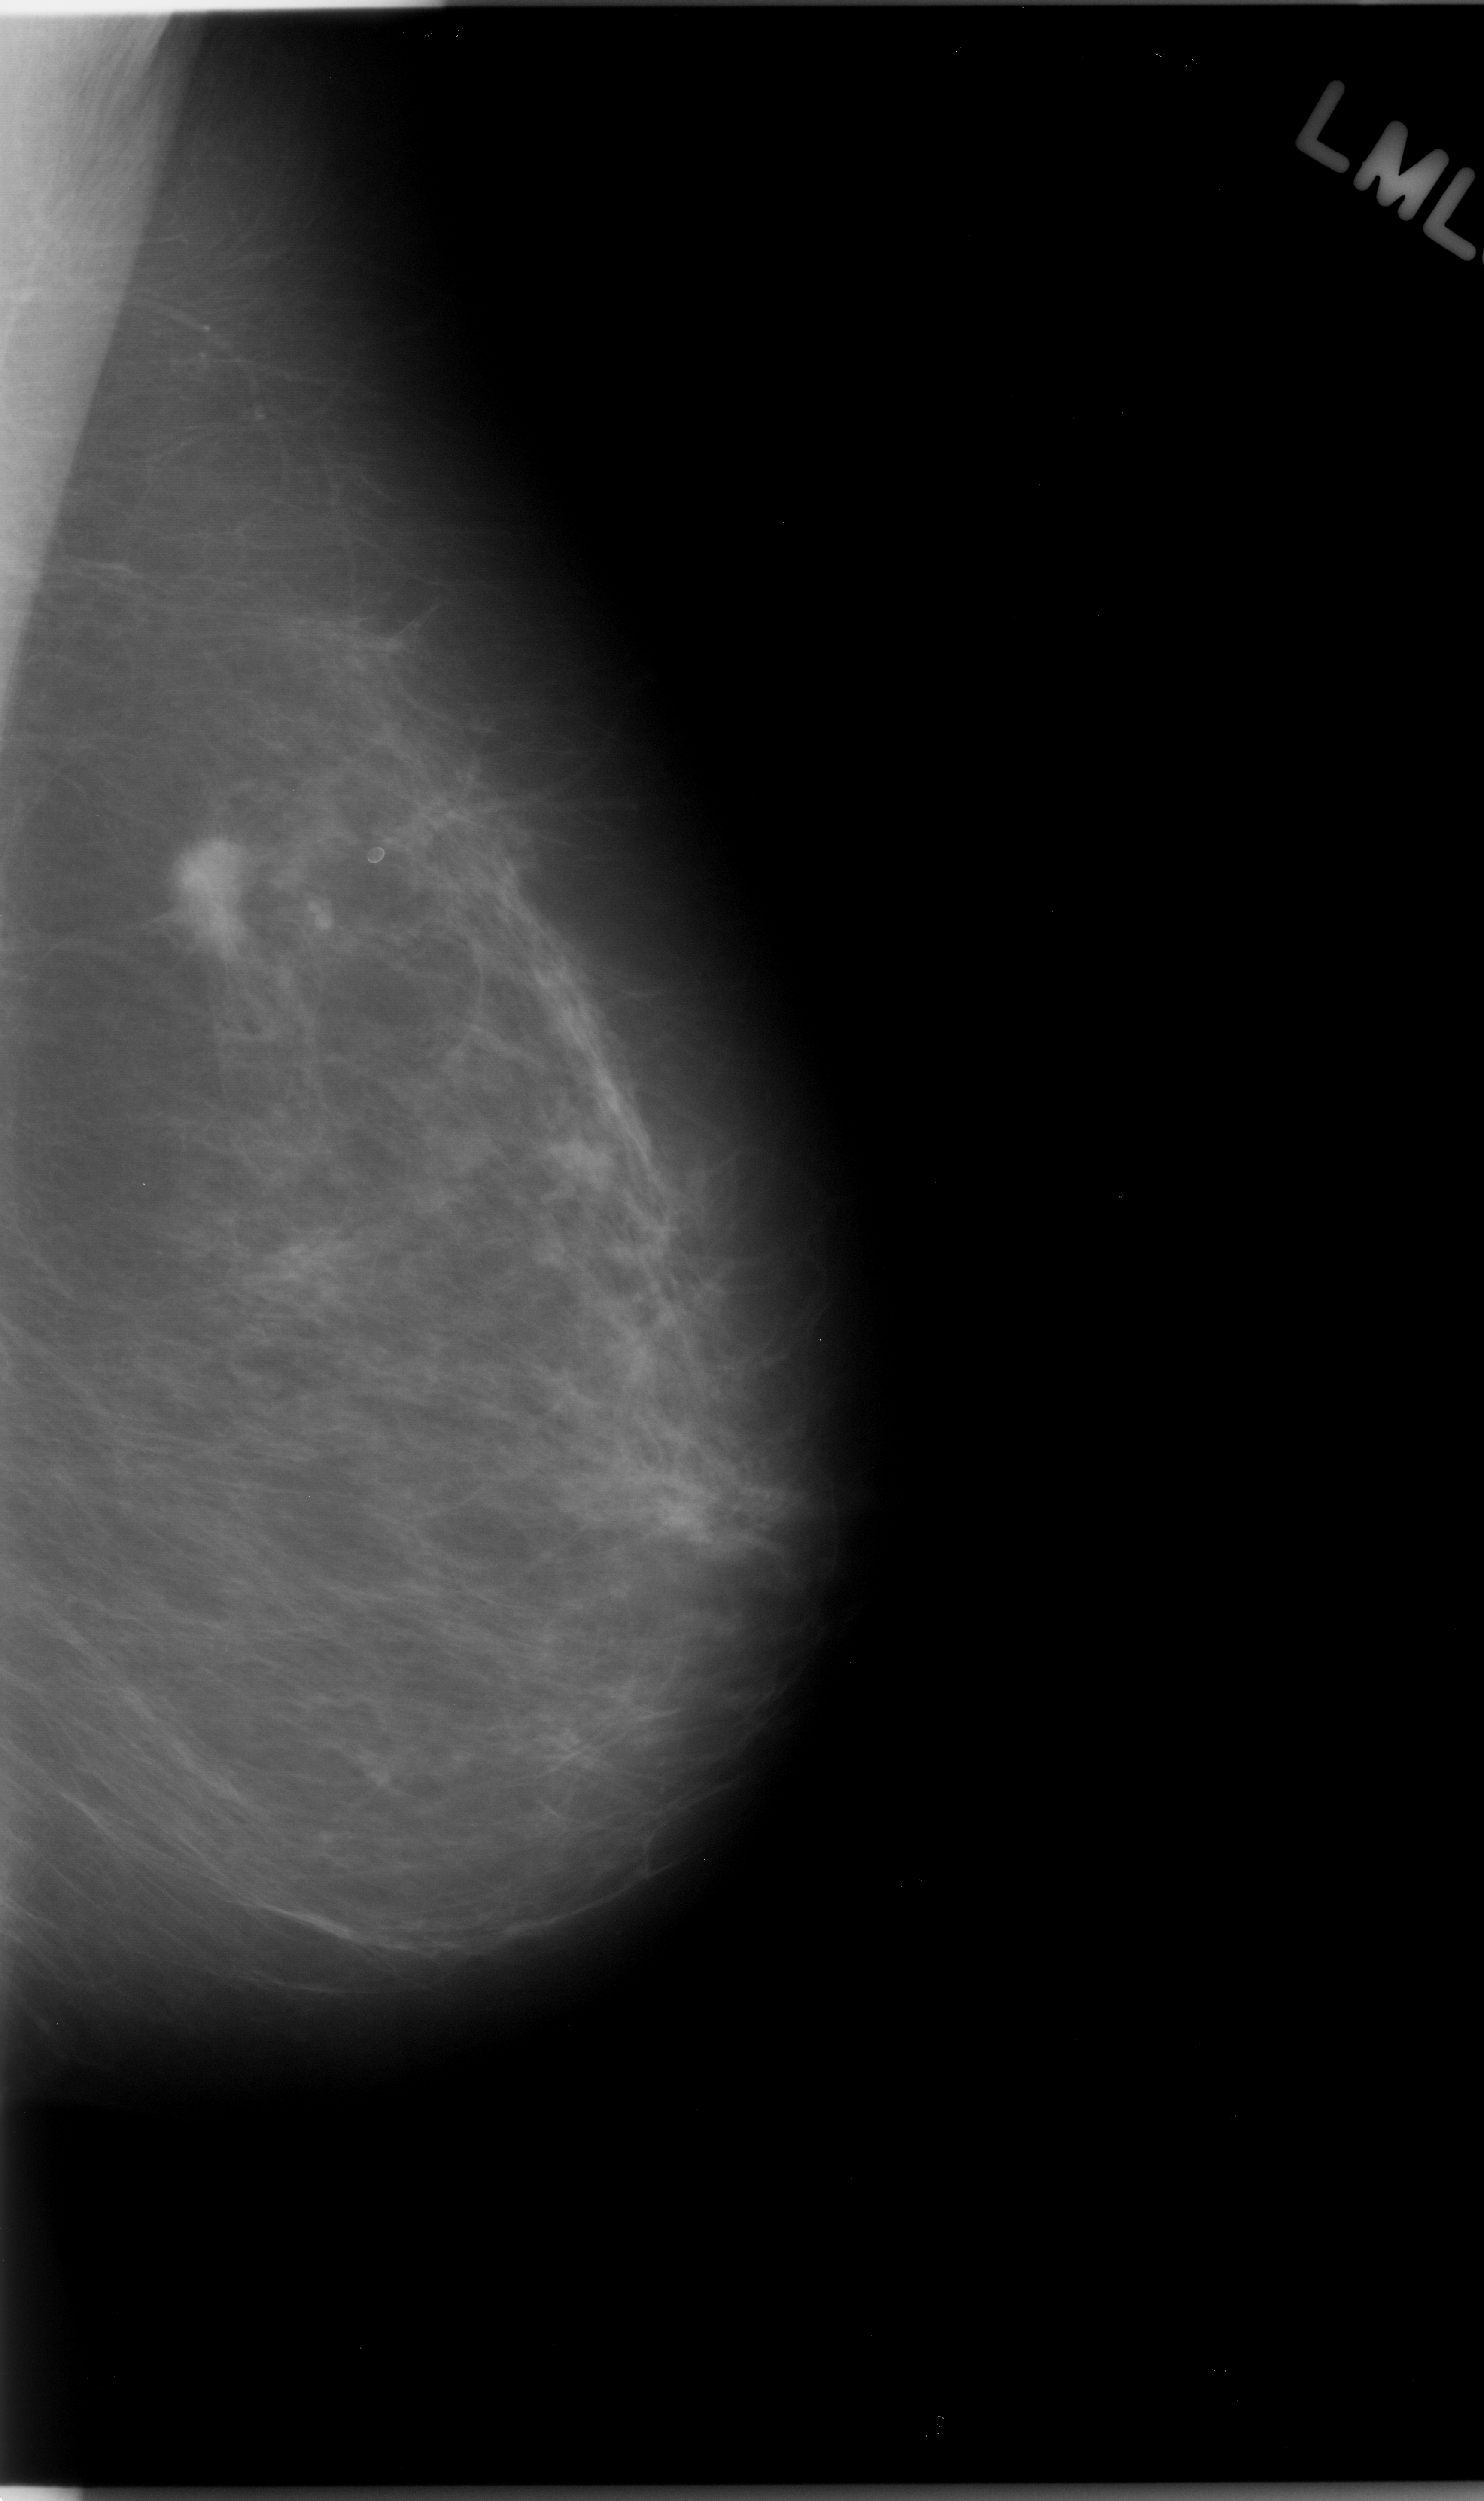
Mammogram (digitized film). Left breast. MLO view. Breast composition: almost entirely fatty (BI-RADS density category 1 of 4). 1484 × 2501 image matrix.
Expert-marked regions of interest on this film, with their recorded descriptors:
- mass, shape lobulated, margins spiculated; BI-RADS assessment category 5; subtlety rating 5 on a 1 (subtle) to 5 (obvious) scale; pathology result (as recorded, not read from the image): malignant: bounding box (x1, y1, x2, y2) in pixels: (161, 814, 276, 962)